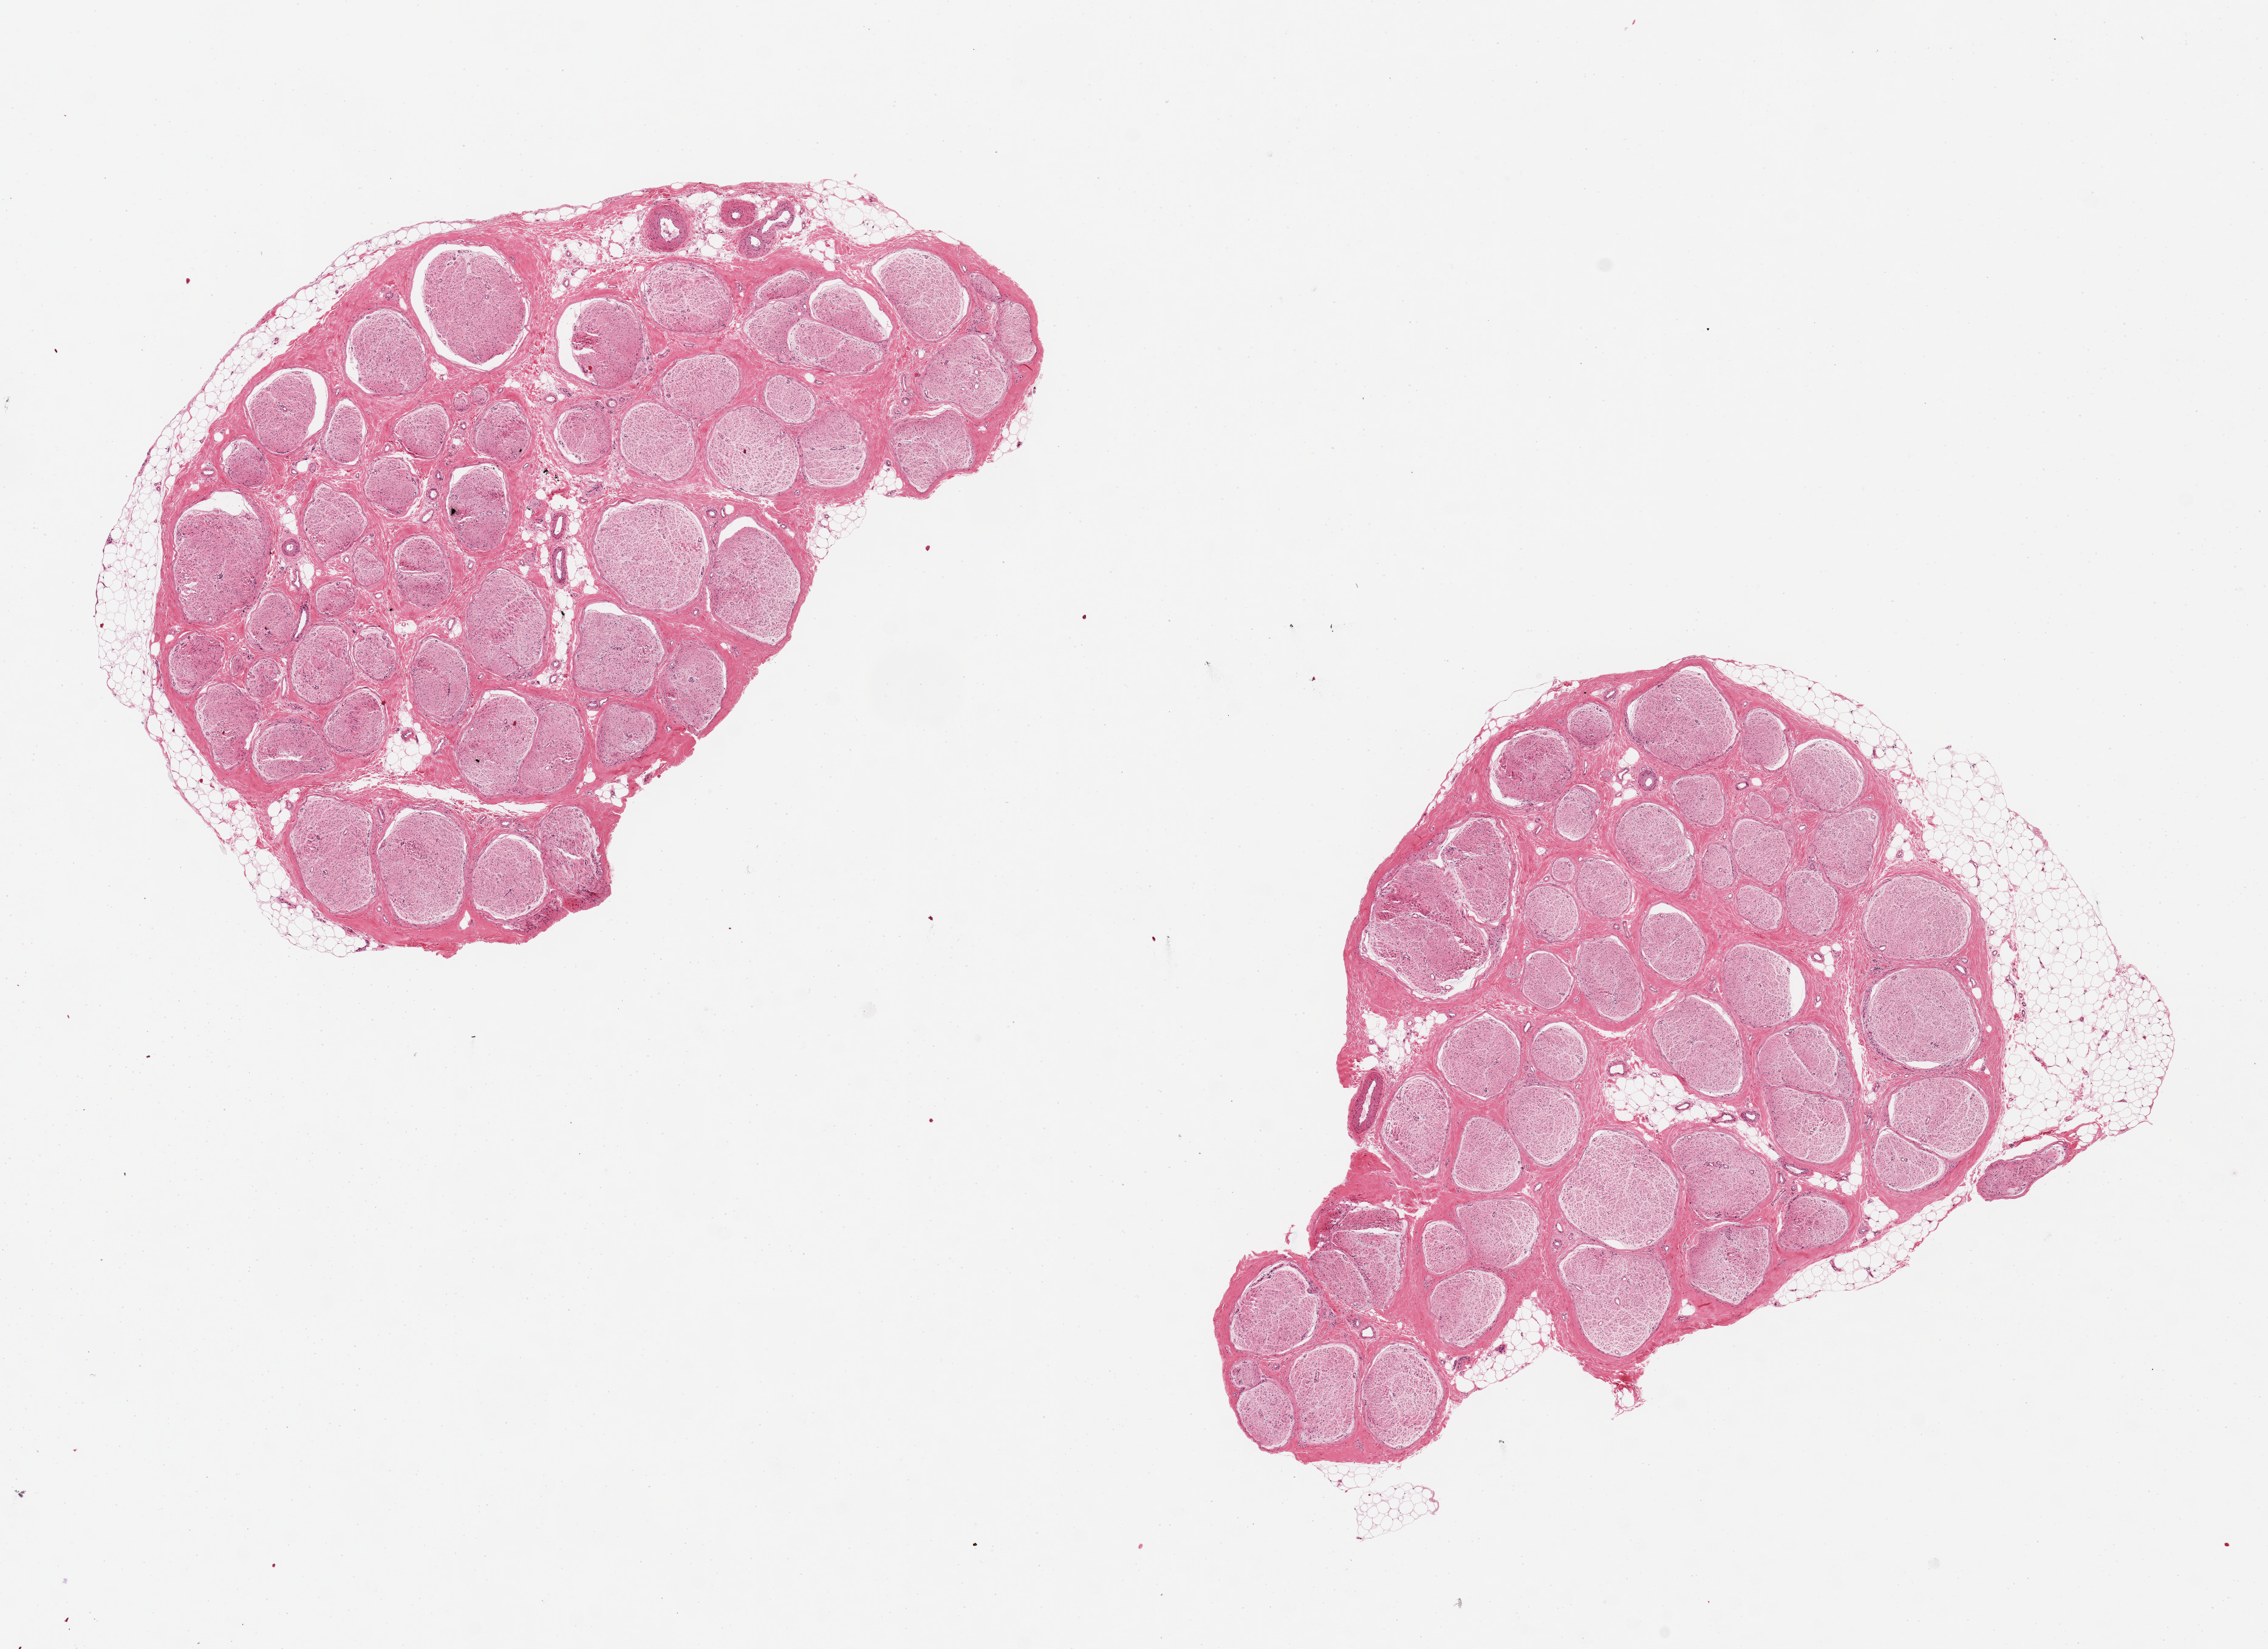
Digitized H&E-stained section — a low-resolution overview of the entire scanned area, about 14.8 x 10.7 mm; PAXgene-fixed, paraffin-embedded tissue; section of tibial nerve (target tissue); donor tissue sample. Donor sex: female.
Reviewer comment on this tissue sample: 2 pieces 6x4 & 6x4 mm; ~10% adipose at periphery of each.